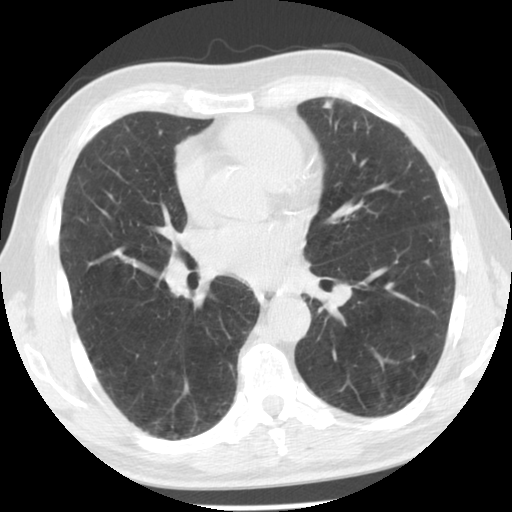
Low-dose screening chest CT, one axial slice; slice 64 of 129 in the series (ordered by position); reconstruction kernel STANDARD; 140 kVp; lung window (W 1500 / L -600 HU); 2.5 mm slice thickness; 512 × 512 image matrix, field of view 330 × 330 mm.
Structures marked on this image (expert manual segmentation):
- lesion 1 (tumor, upper lobe of left lung): bounding box (x1, y1, x2, y2) in pixels: (323, 99, 334, 109)